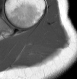
MRI of an extremity soft-tissue mass, one axial slice. Position 20 of 28 along the scan axis. MR volume resampled by the dataset authors to the PET/CT grid (not the native acquisition matrix). 3.27 mm slice thickness. 77 × 79 image matrix, field of view 75 × 77 mm. Female patient. From the clinical record (not read from this slice): histological type: malignant fibrous histiocytoma; grade: low; site of the primary tumour: left arm.
Annotated regions visible in this slice (expert contour drawn on MRI and transferred to this co-registered scan by the dataset authors):
- gross tumour volume (mass): bounding box <24,45,41,55> (left, top, right, bottom; pixels)